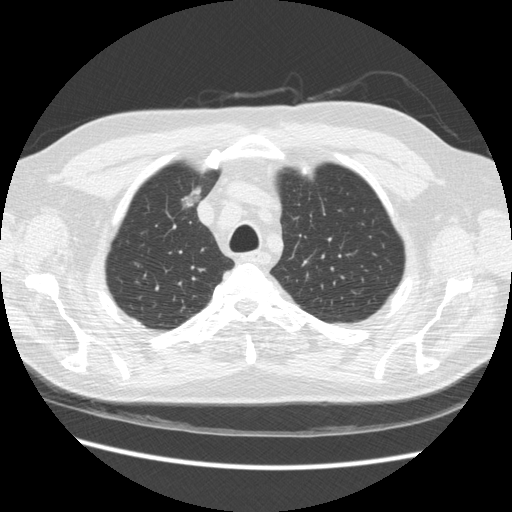
Low-dose screening chest CT, one axial slice; slice 186 of 234 in the series (ordered by position); reconstruction kernel STANDARD; 120 kVp; lung window (W 1500 / L -600 HU); 2.5 mm slice thickness; 512 × 512 image matrix.
Structures marked on this image (outlined manually by an expert reader):
- lesion 1 (tumor, upper lobe of right lung): bounding box <181,186,201,208> (left, top, right, bottom; pixels)